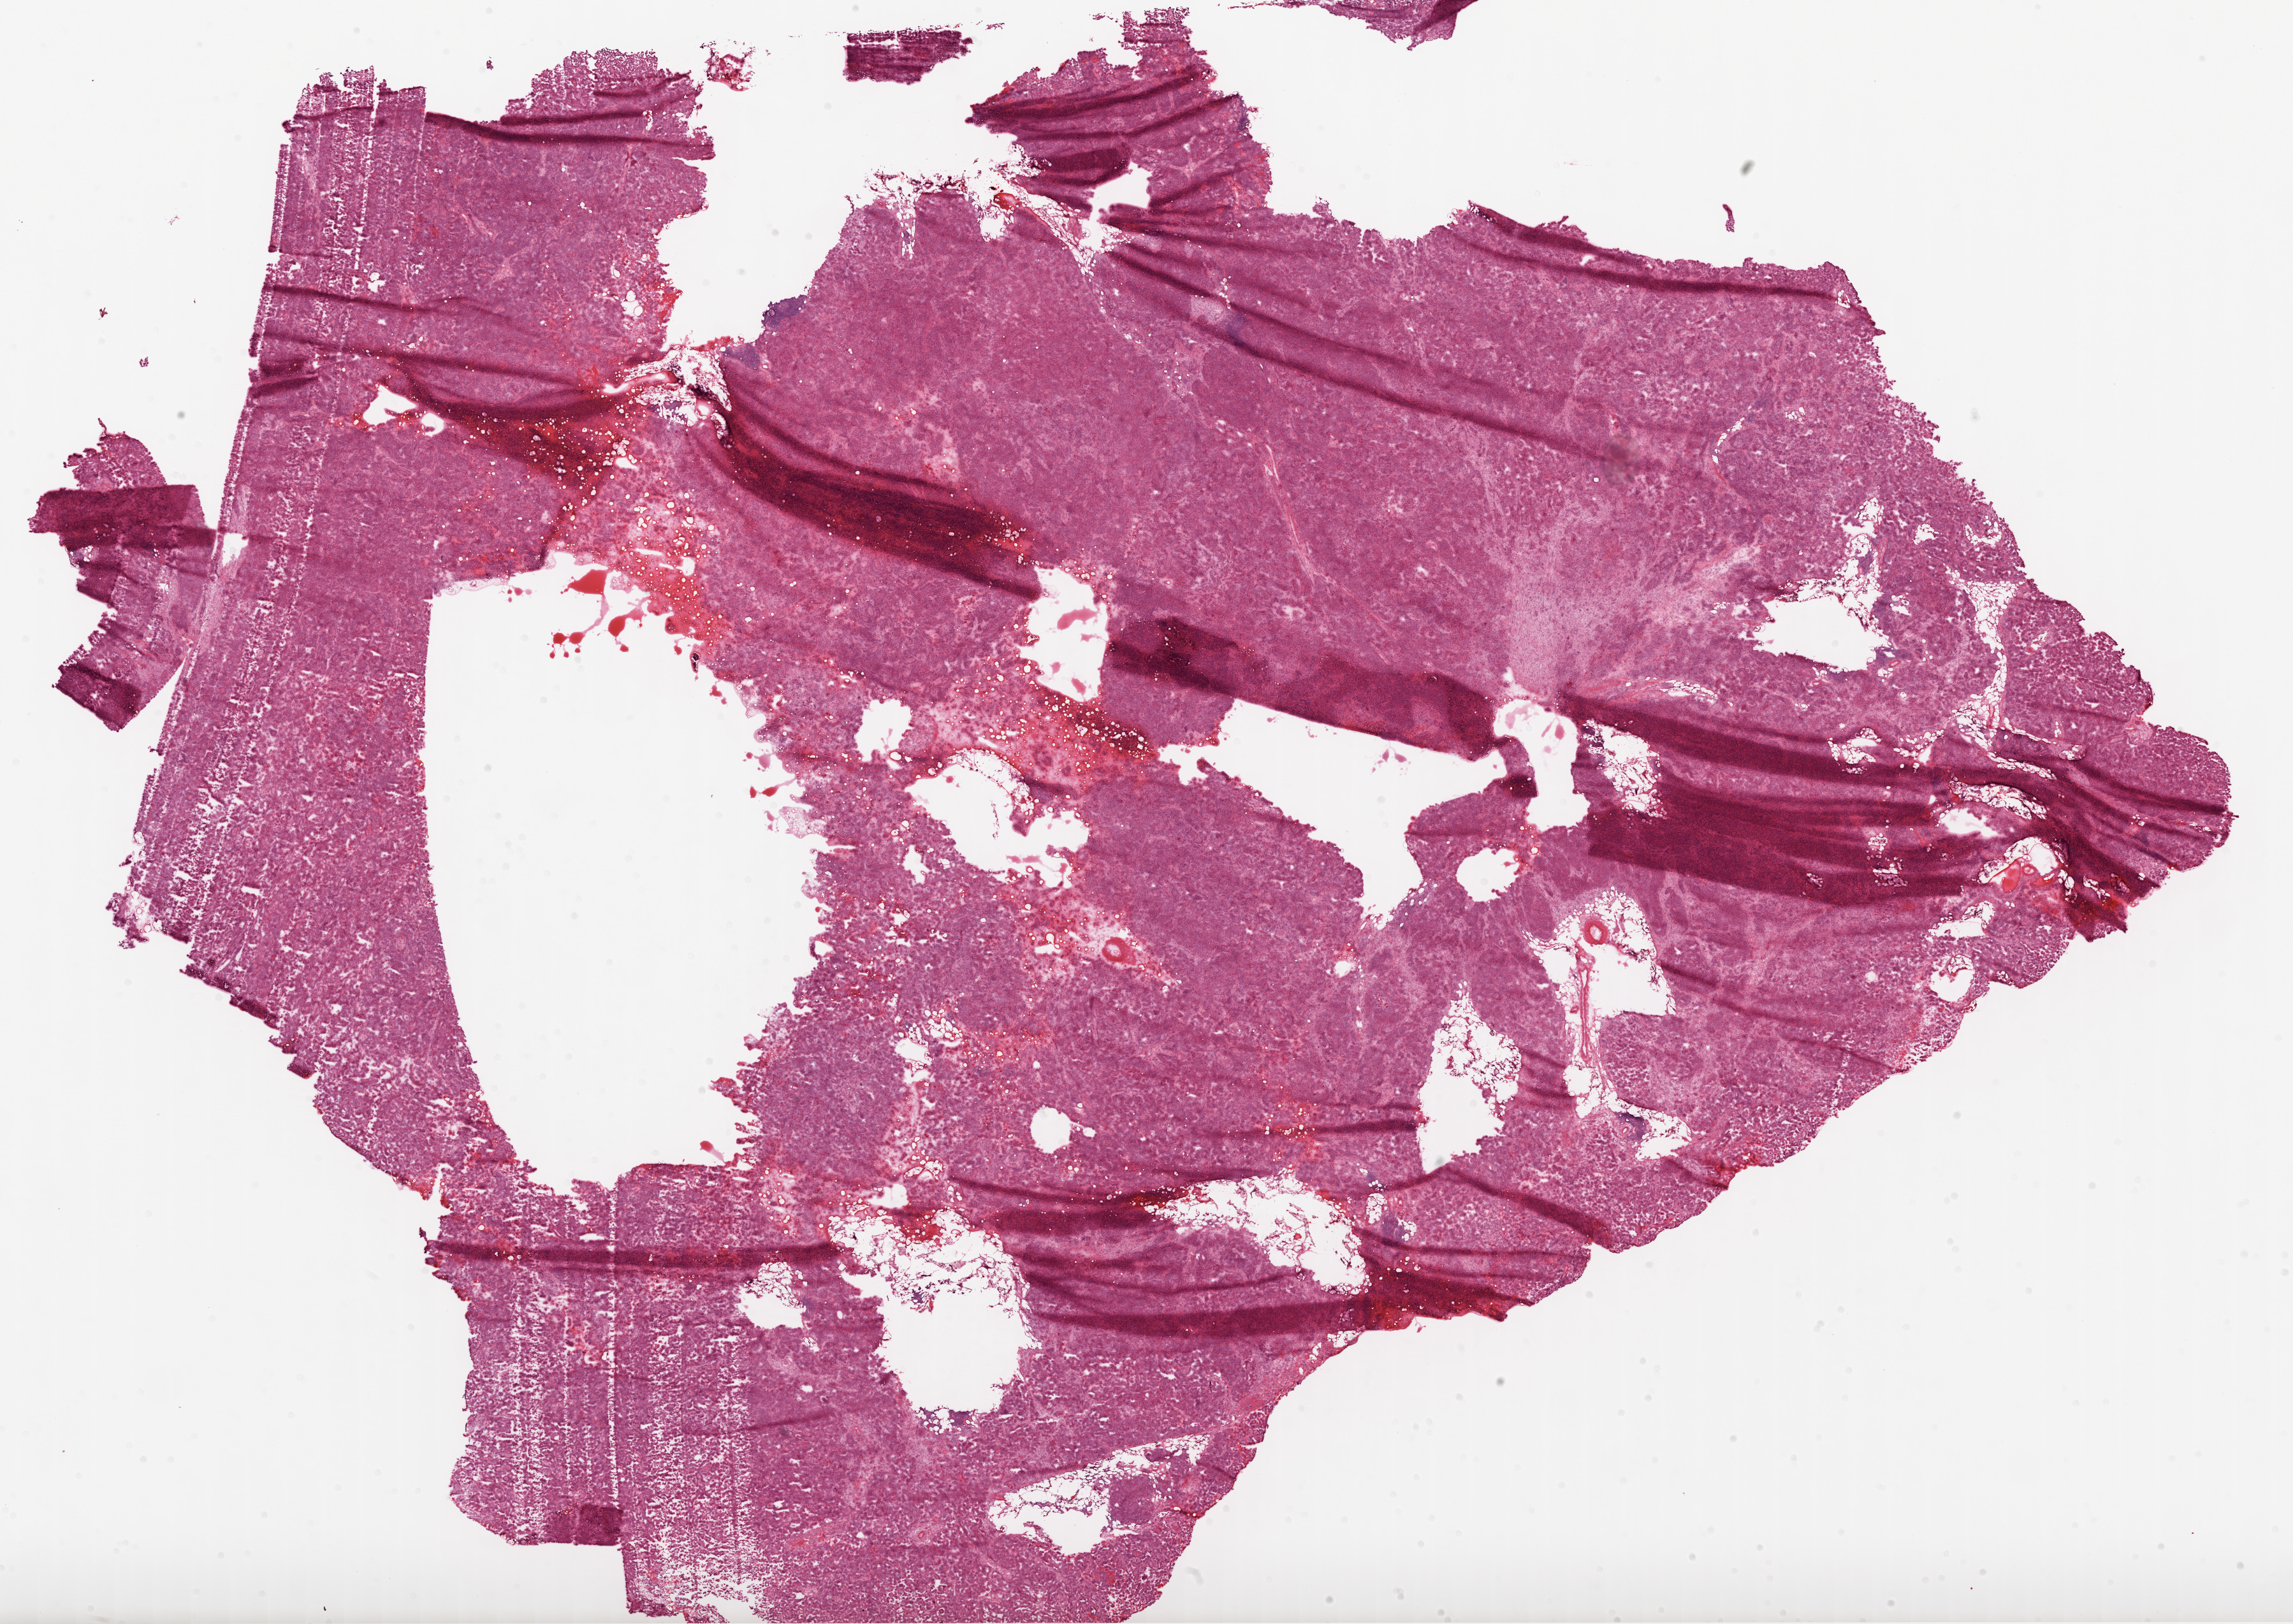
Digitized H&E tissue section (whole slide) — whole scanned area (about 29.0 x 20.5 mm, slide scanned at 20x) shown as a low-resolution overview, frozen section, primary tumour sample from the ovary. Female, age 42 years at initial diagnosis. Histologic grade: G3 (poorly differentiated). Slide review estimates, as recorded: tumour cells 98%, tumour nuclei 98%, normal cells 0%, stromal cells 2%, necrosis 0%.
* laterality: bilateral
* FIGO stage: IV
* diagnosis: Serous cystadenocarcinoma, NOS